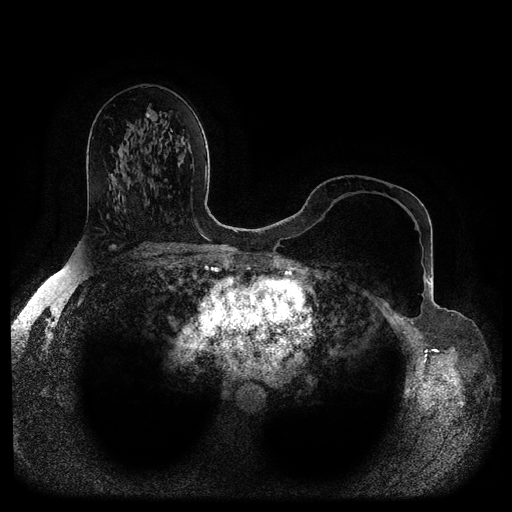
Breast MRI (dynamic contrast-enhanced, multi-phase), one axial slice; slice 54 of 116 in the series (ordered by position); dynamic contrast-enhanced series, time point 2 of 5 at this slice position (early post-contrast); 1.5 T; TE 2.6 ms, TR 5.2 ms; 2 mm slice thickness; 512 × 512 image matrix, field of view 380 × 380 mm. Female patient, age 56 years.
Structures marked on this image (semi-automatically segmented with operator editing):
- breast lesion (labelled benign in the annotation): bounding box [x1, y1, x2, y2] px = [146, 113, 150, 118]